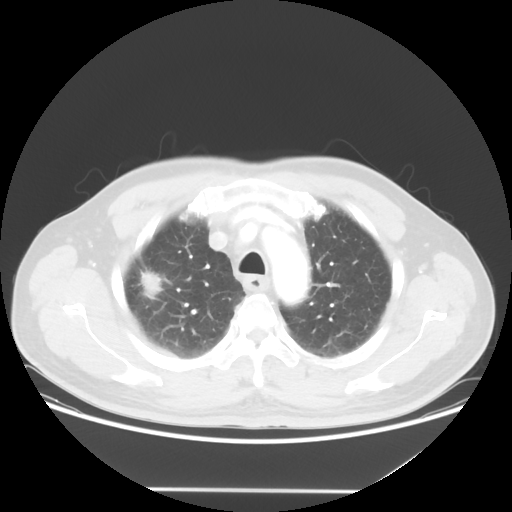
Chest CT, one axial slice; position 42 of 54 along the scan axis; 120 kVp; lung window (W 1500 / L -600 HU); 512 × 512 image matrix, field of view 416 × 416 mm. Patient: male, 65 years. From the clinical record (not read from this slice): clinical TNM (as recorded): T1c N1 M0.
Outlined on this slice (bounding box drawn by a radiologist):
- lung tumour (recorded histology: adenocarcinoma): bounding box (x1, y1, x2, y2) in pixels: (134, 266, 166, 305)